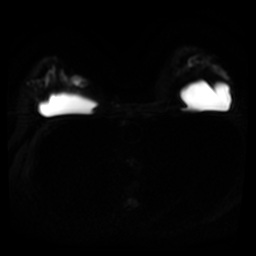
Breast MRI, one axial slice; position 29 of 45 along the scan axis; diffusion-weighted series; image 2 of 4 stored at this slice position (different b-values; order by instance number); 3 T; 5 mm slice thickness; 256 × 256 image matrix, field of view 320 × 320 mm. Female patient.
Outlined on this slice (manually delineated by an expert):
- tumour on diffusion-weighted imaging: bounding box [x1, y1, x2, y2] px = [73, 77, 81, 86]